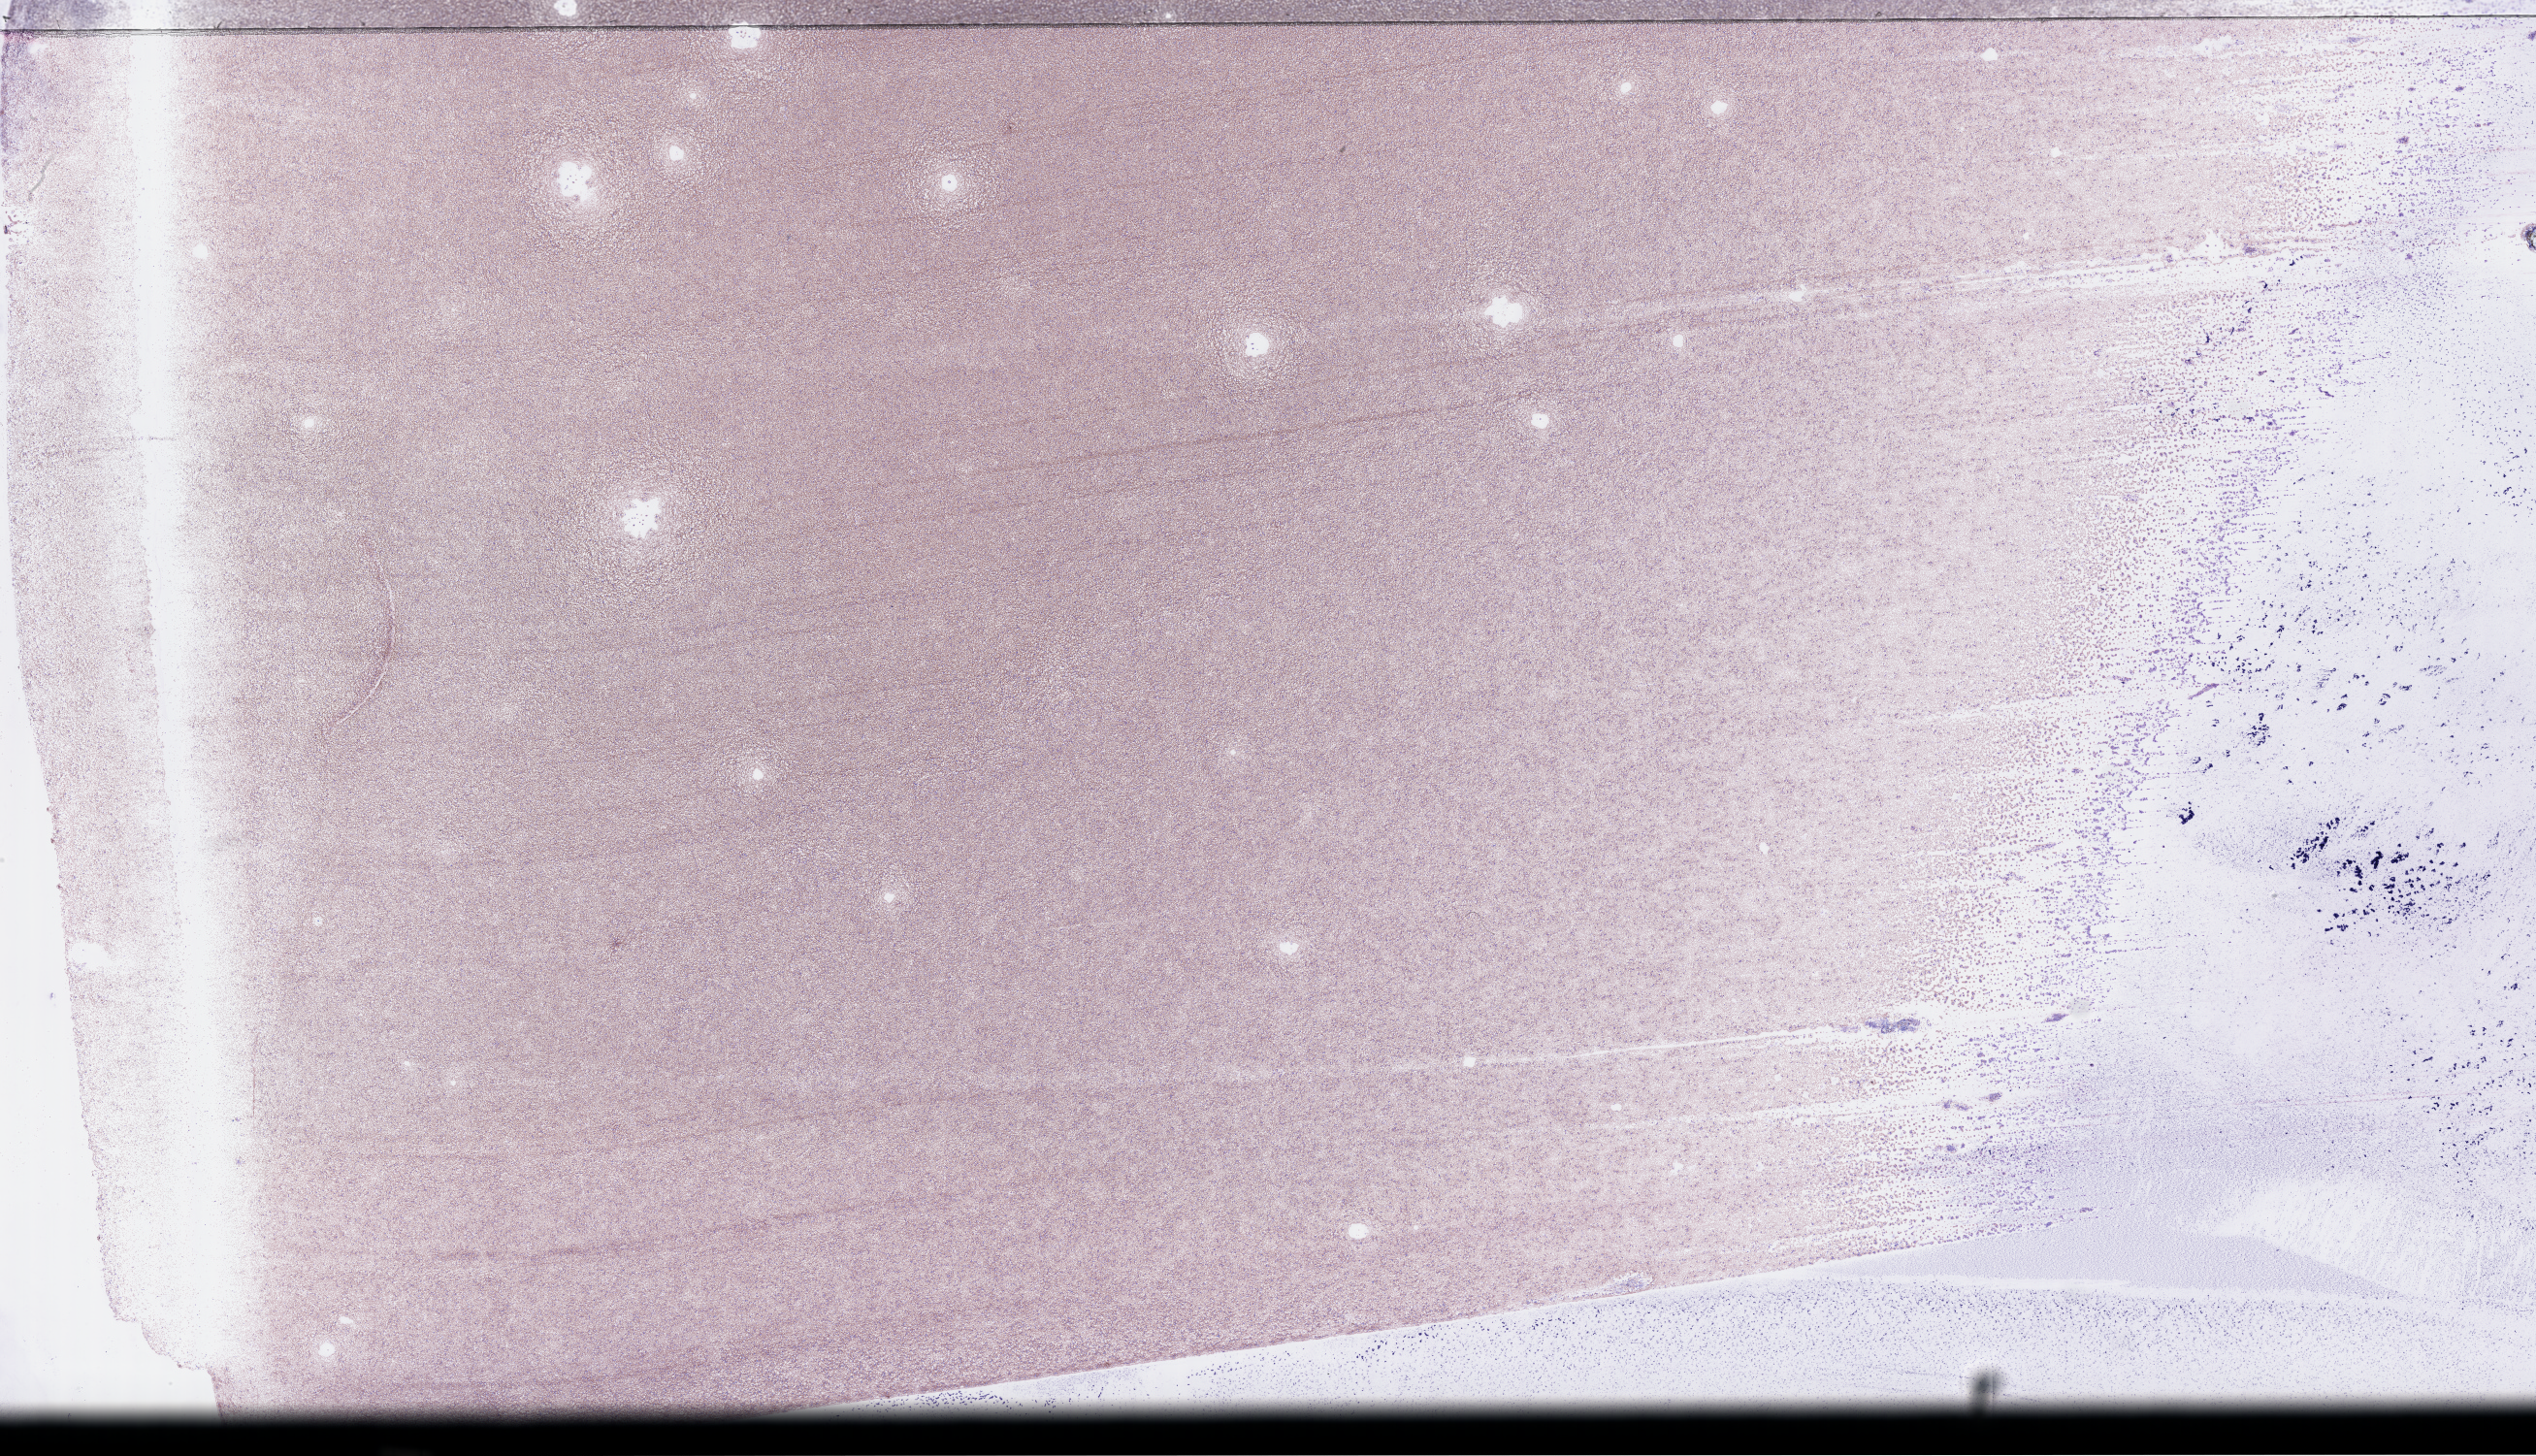
Whole-slide image of a bone marrow smear, Wright–Giemsa stain, low-resolution overview of the scanned area, about 42.2 x 24.2 mm. EDTA-anticoagulated smear. Patient: female.
From a patient with: Acute Myeloid Leukemia Not Otherwise Specified.